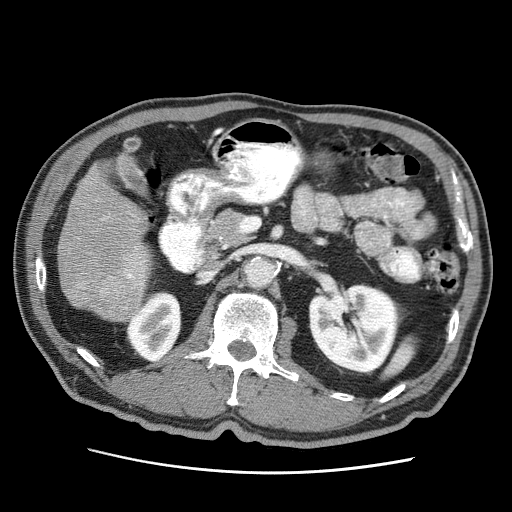
Contrast-enhanced abdominal CT (liver protocol), one axial slice. Slice 13 of 75 in the series (ordered by position). Soft-tissue window (W 400 / L 40 HU). 512 × 512 image matrix, field of view 360 × 360 mm. From the clinical record (not read from this slice): diagnosis: hepatocellular carcinoma (patient treated with transarterial chemoembolisation; whether this scan precedes or follows treatment is not stated here); TNM stage (as recorded): Stage-IIIA; Child-Pugh class: A; tumour differentiation: well differentiated.
Structures marked on this image (semi-automatically segmented with operator editing):
- liver parenchyma outside the tumour (the mass and vessels are separate outlines, so this box may not span the whole liver): bounding box (x1, y1, x2, y2) in pixels: (58, 165, 150, 320)
- mass: (58, 167, 138, 298)
- liver vessels: (125, 246, 142, 279)